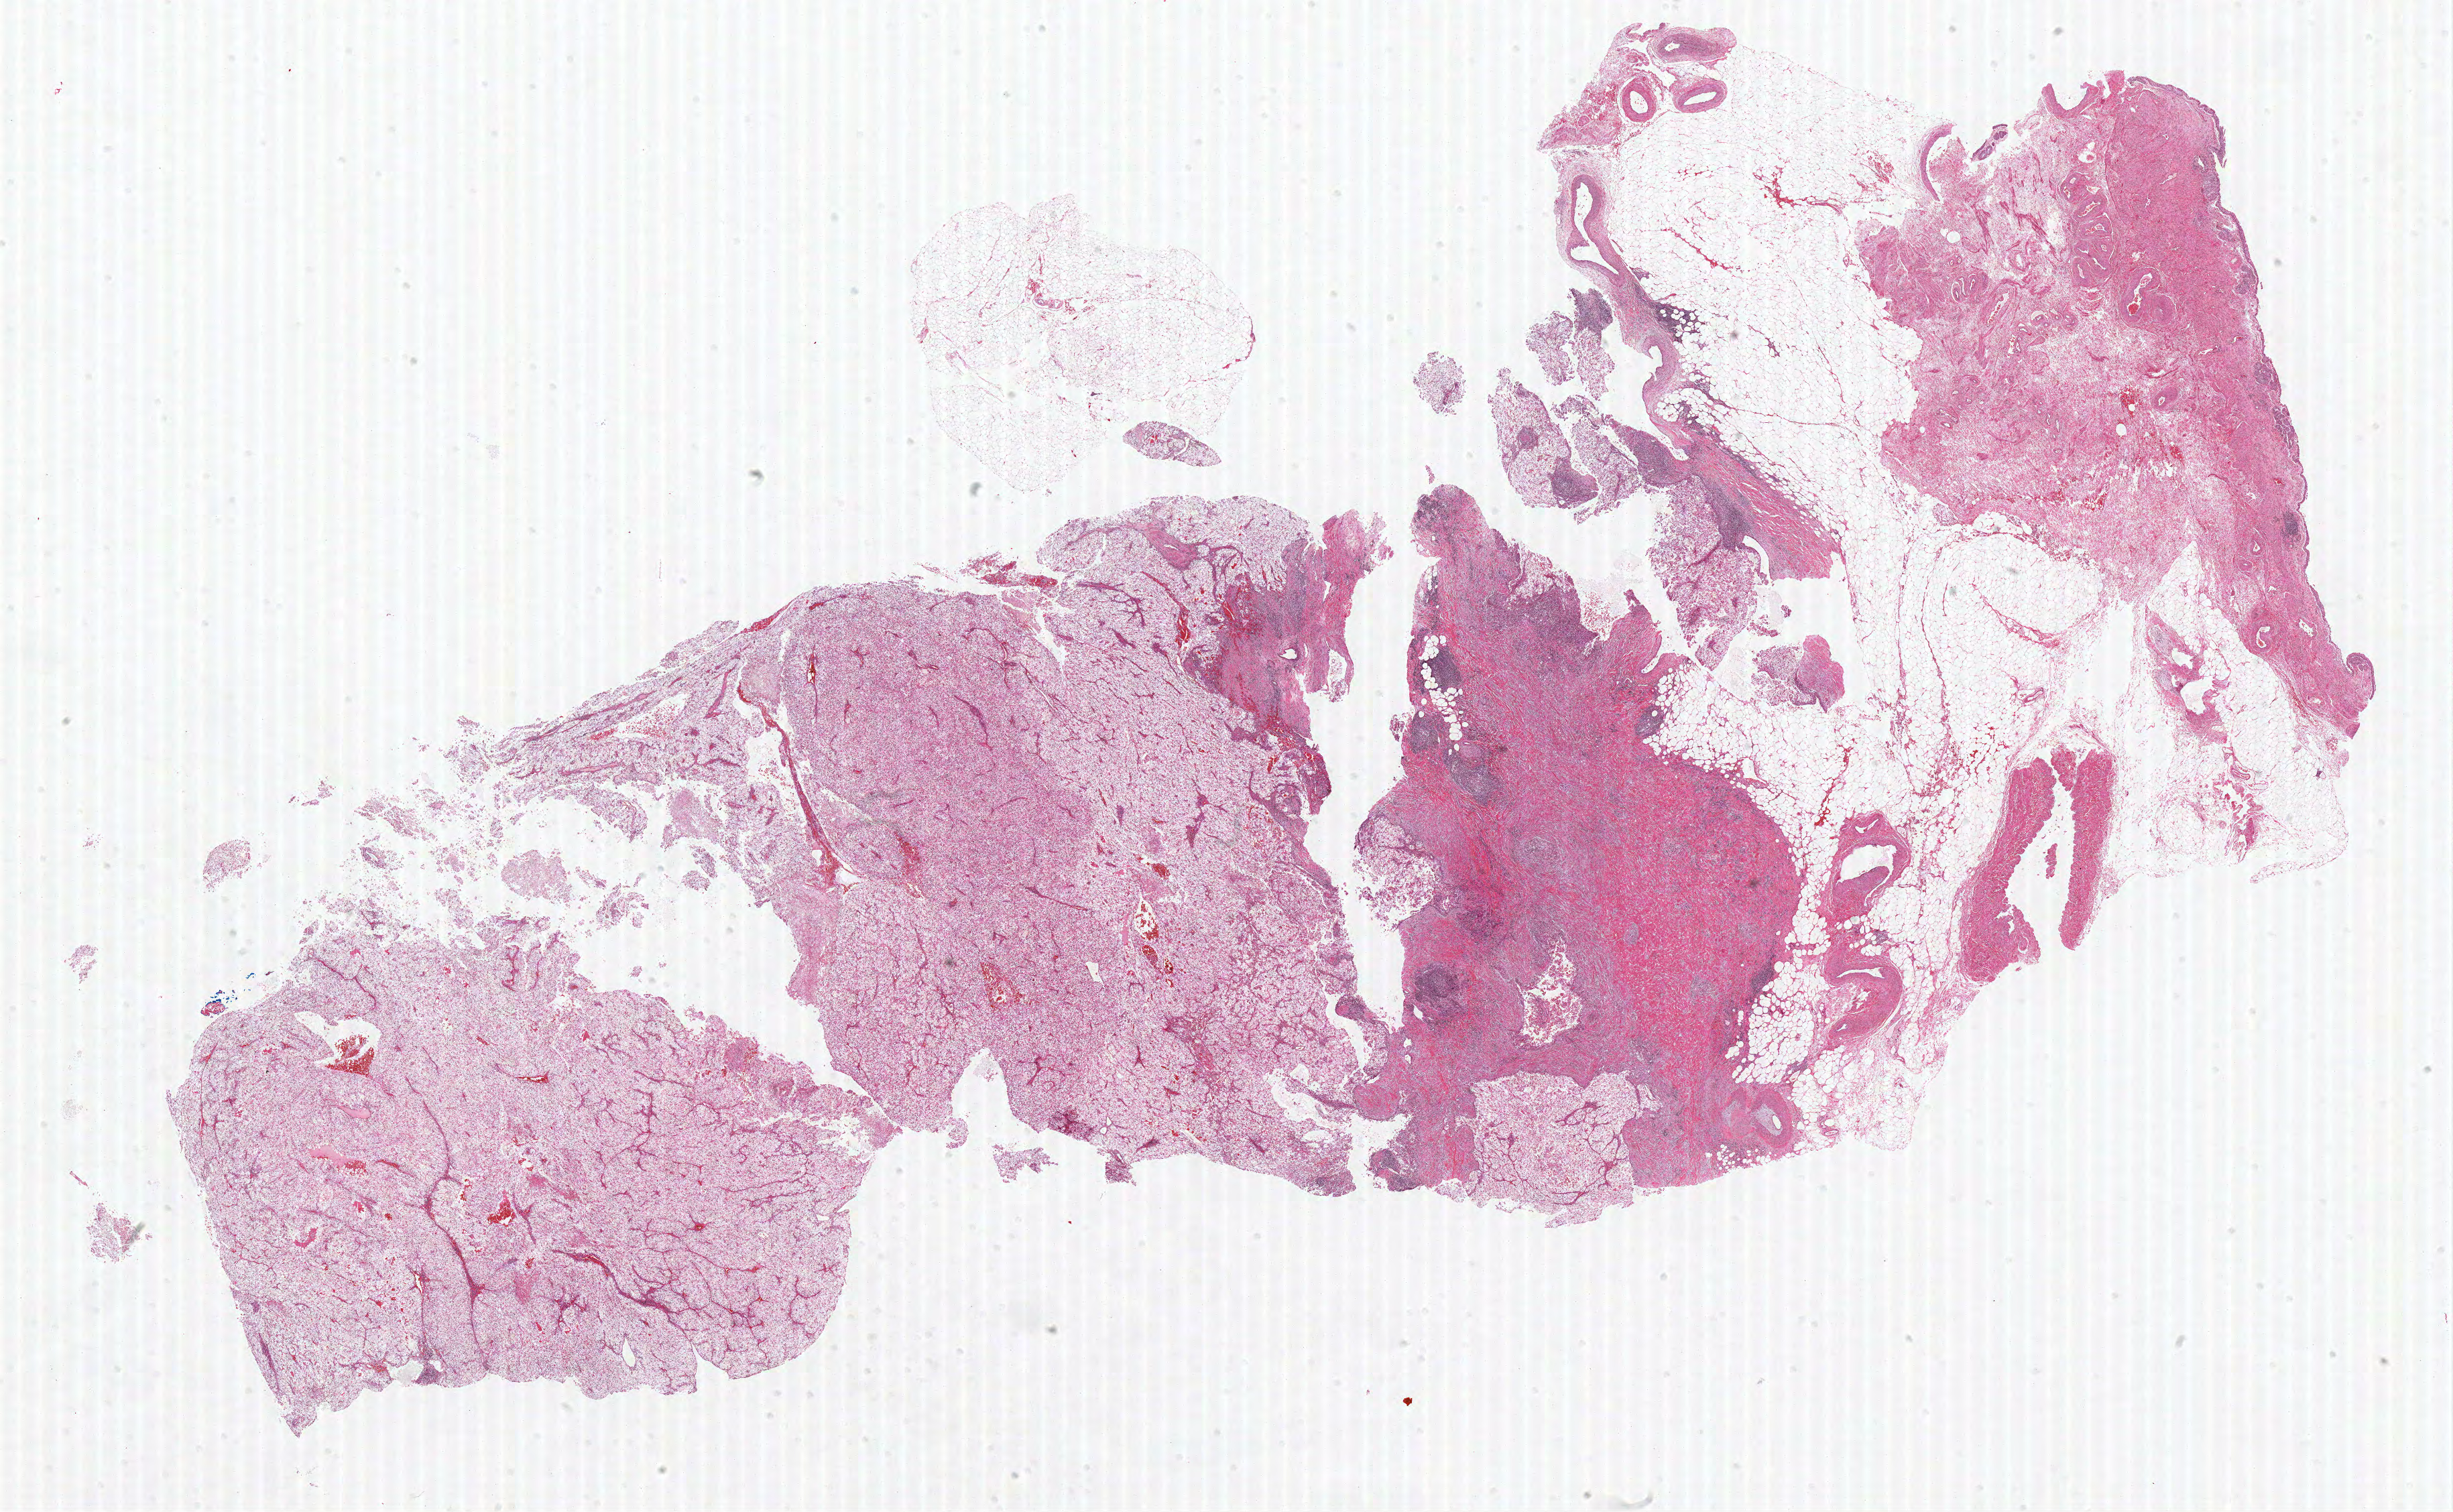
Digitized H&E tissue section (whole slide), whole scanned area (about 29.3 x 18.0 mm) shown as a low-resolution overview, formalin-fixed paraffin-embedded (FFPE) diagnostic section, primary tumour sample from the kidney. Male, age 74 years at initial diagnosis. Histologic grade: G3 (poorly differentiated).
Diagnosis: Clear cell adenocarcinoma, NOS. AJCC pathologic stage: I.